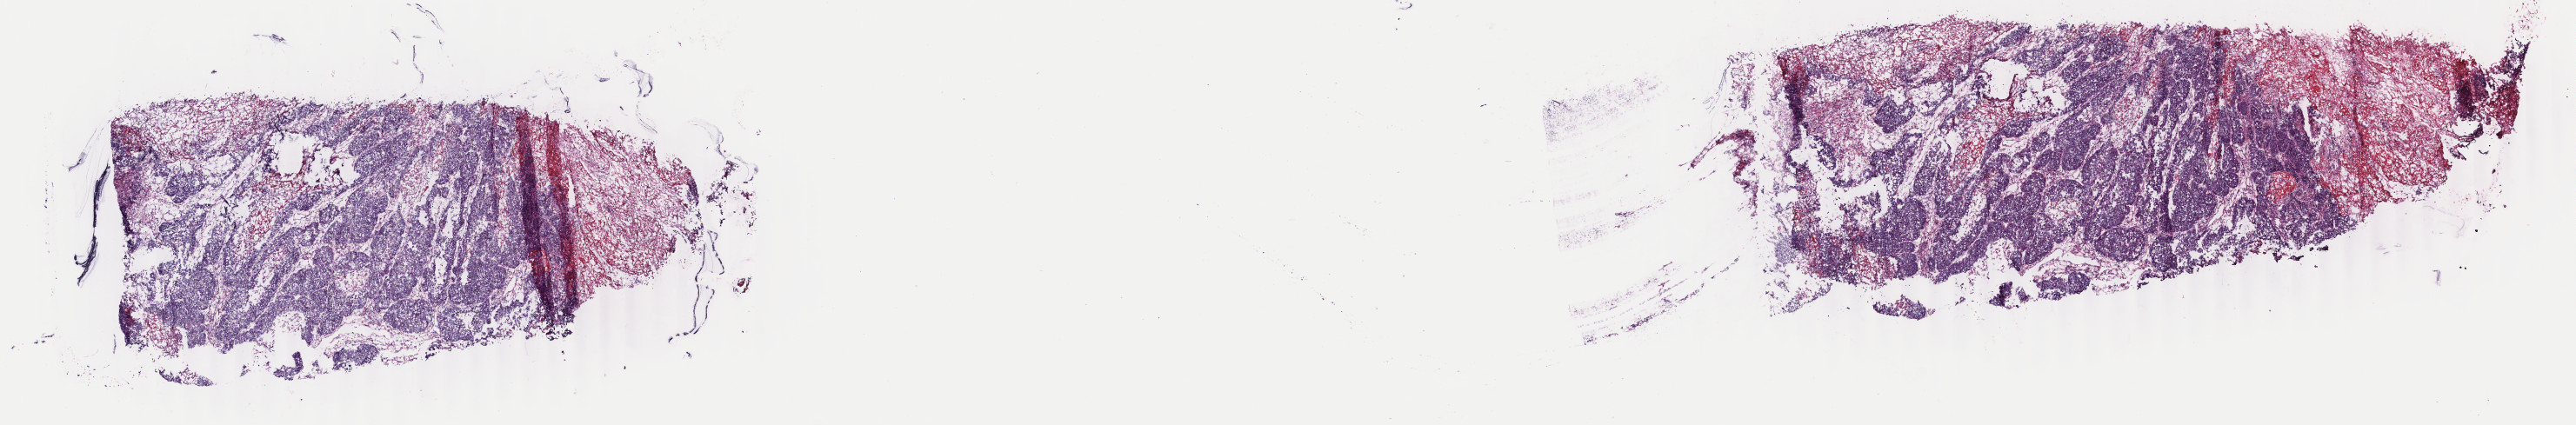
H&E-stained whole-slide image — shown as a low-resolution overview of the whole scanned area (about 23.6 x 3.9 mm). Frozen section. Metastatic tumour sample. Female patient; age at initial diagnosis 34 years. Slide review estimates, as recorded: tumour cells 60%, tumour nuclei 60%.
This section: metastatic tumour tissue. Patient diagnosis: Squamous cell carcinoma, NOS (primary site: ovary).